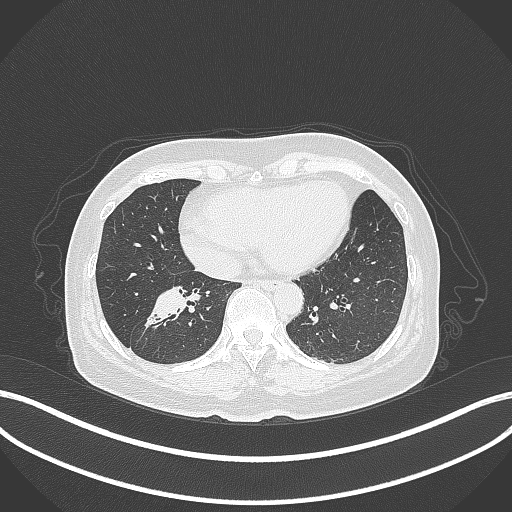
Chest CT, one axial slice; reconstruction kernel B70f; 120 kVp; lung window (W 1500 / L -600 HU); 1 mm slice thickness; 512 × 512 image matrix. Female patient, age 67 years. Case-level facts recorded for this patient, not image findings: clinical TNM (as recorded): T1c N1 M0.
Annotated regions visible in this slice (rectangle marked by the reading radiologist):
- lung tumour (recorded histology: adenocarcinoma): bounding box <138,285,188,327> (left, top, right, bottom; pixels)